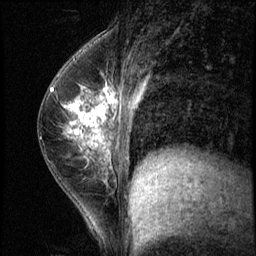
Breast MRI (dynamic contrast-enhanced), one sagittal slice. Position 30 of 56 along the scan axis. 3 images stored at this slice position (order not interpretable as contrast timing). 1.5 T. TE 4.2 ms, TR 8.7 ms. 2.5 mm slice thickness. 256 × 256 image matrix, field of view 180 × 180 mm. Patient: female, 35 years. Case-level facts recorded for this patient, not image findings: setting: breast cancer imaged before/during neoadjuvant chemotherapy; receptor status: HER2-positive.
Outlined on this slice (semi-automatically segmented with operator editing):
- analysis volume of interest (the breast-tissue region the enhancement analysis was run in; not a lesion): bounding box (x1, y1, x2, y2) in pixels: (58, 84, 138, 186)
- tumour enhancement mask (voxels above the 140 % enhancement threshold inside the analysis volume of interest): (63, 87, 114, 149)